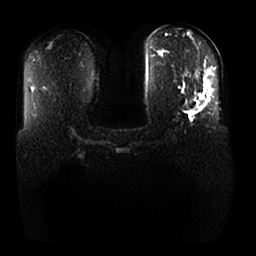
Breast MRI, one axial slice; position 13 of 25 along the scan axis; diffusion-weighted series; image 2 of 4 stored at this slice position (different b-values; order by instance number); 1.5 T; 4 mm slice thickness; 256 × 256 image matrix, field of view 370 × 370 mm. Female patient.
Annotated regions visible in this slice (expert manual segmentation):
- tumour on diffusion-weighted imaging: bounding box (x1, y1, x2, y2) in pixels: (202, 83, 211, 106)